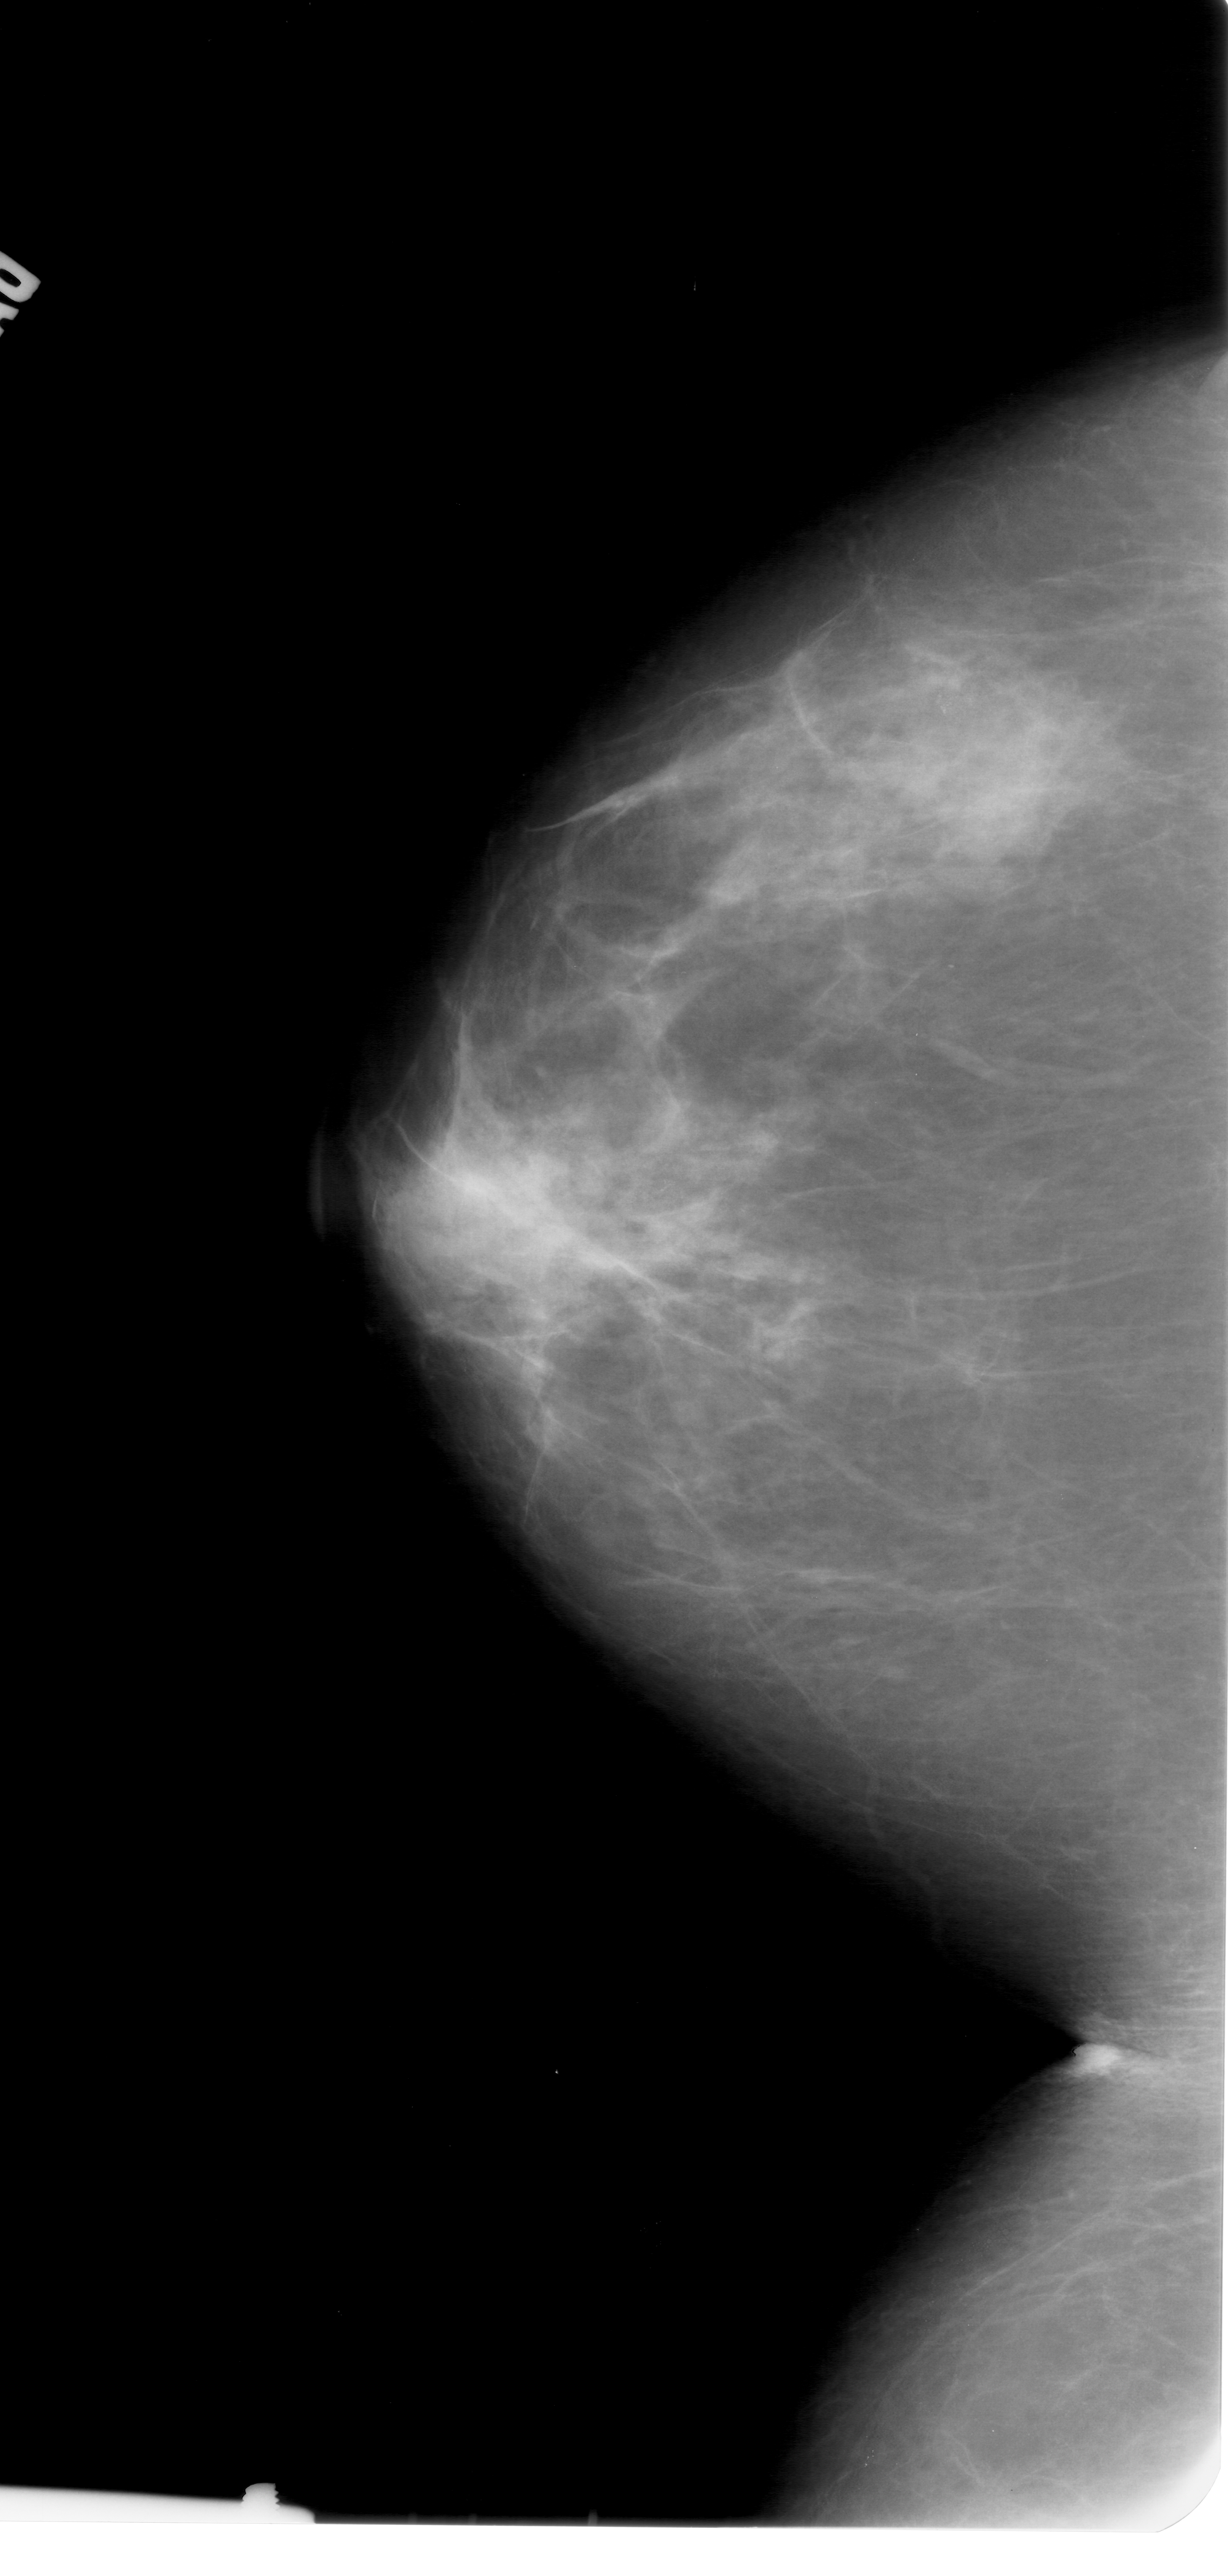
Digitized screen-film mammogram, left breast, craniocaudal (CC) view, BI-RADS breast density category 3 (scale 1–4).
Calcifications, morphology pleomorphic, distribution clustered; BI-RADS assessment category 4; pathology (as recorded): malignant.